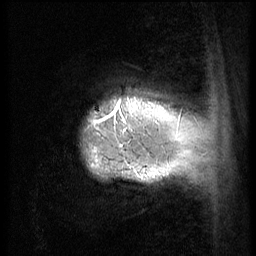
Breast MRI (dynamic contrast-enhanced), one sagittal slice. Position 6 of 56 along the scan axis. 3 images stored at this slice position (order not interpretable as contrast timing). 1.5 T. TE 4.2 ms, TR 9 ms. 2.5 mm slice thickness. 256 × 256 image matrix, field of view 180 × 180 mm. Patient: female, 49 years. Case-level facts recorded for this patient, not image findings: setting: breast cancer imaged before/during neoadjuvant chemotherapy; receptor status: HER2-positive.
Structures marked on this image (semi-automatically segmented with operator editing):
- analysis volume of interest (the breast-tissue region the enhancement analysis was run in; not a lesion): box from (x=66, y=79) to (x=152, y=203) px
- tumour enhancement mask (voxels above the 140 % enhancement threshold inside the analysis volume of interest): (x=91, y=102)–(x=121, y=167)